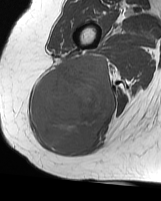
MRI of an extremity soft-tissue mass, one axial slice. Position 32 of 70 along the scan axis. MR volume resampled by the dataset authors to the PET/CT grid (not the native acquisition matrix). 161 × 201 image matrix. Female patient. Case-level facts recorded for this patient, not image findings: histological type: synovial sarcoma; grade: intermediate; site of the primary tumour: right buttock.
Outlined on this slice (expert contour drawn on MRI and transferred to this co-registered scan by the dataset authors):
- gross tumour volume including surrounding oedema: bounding box [x1, y1, x2, y2] px = [33, 54, 116, 155]
- gross tumour volume (mass): [33, 54, 116, 155]